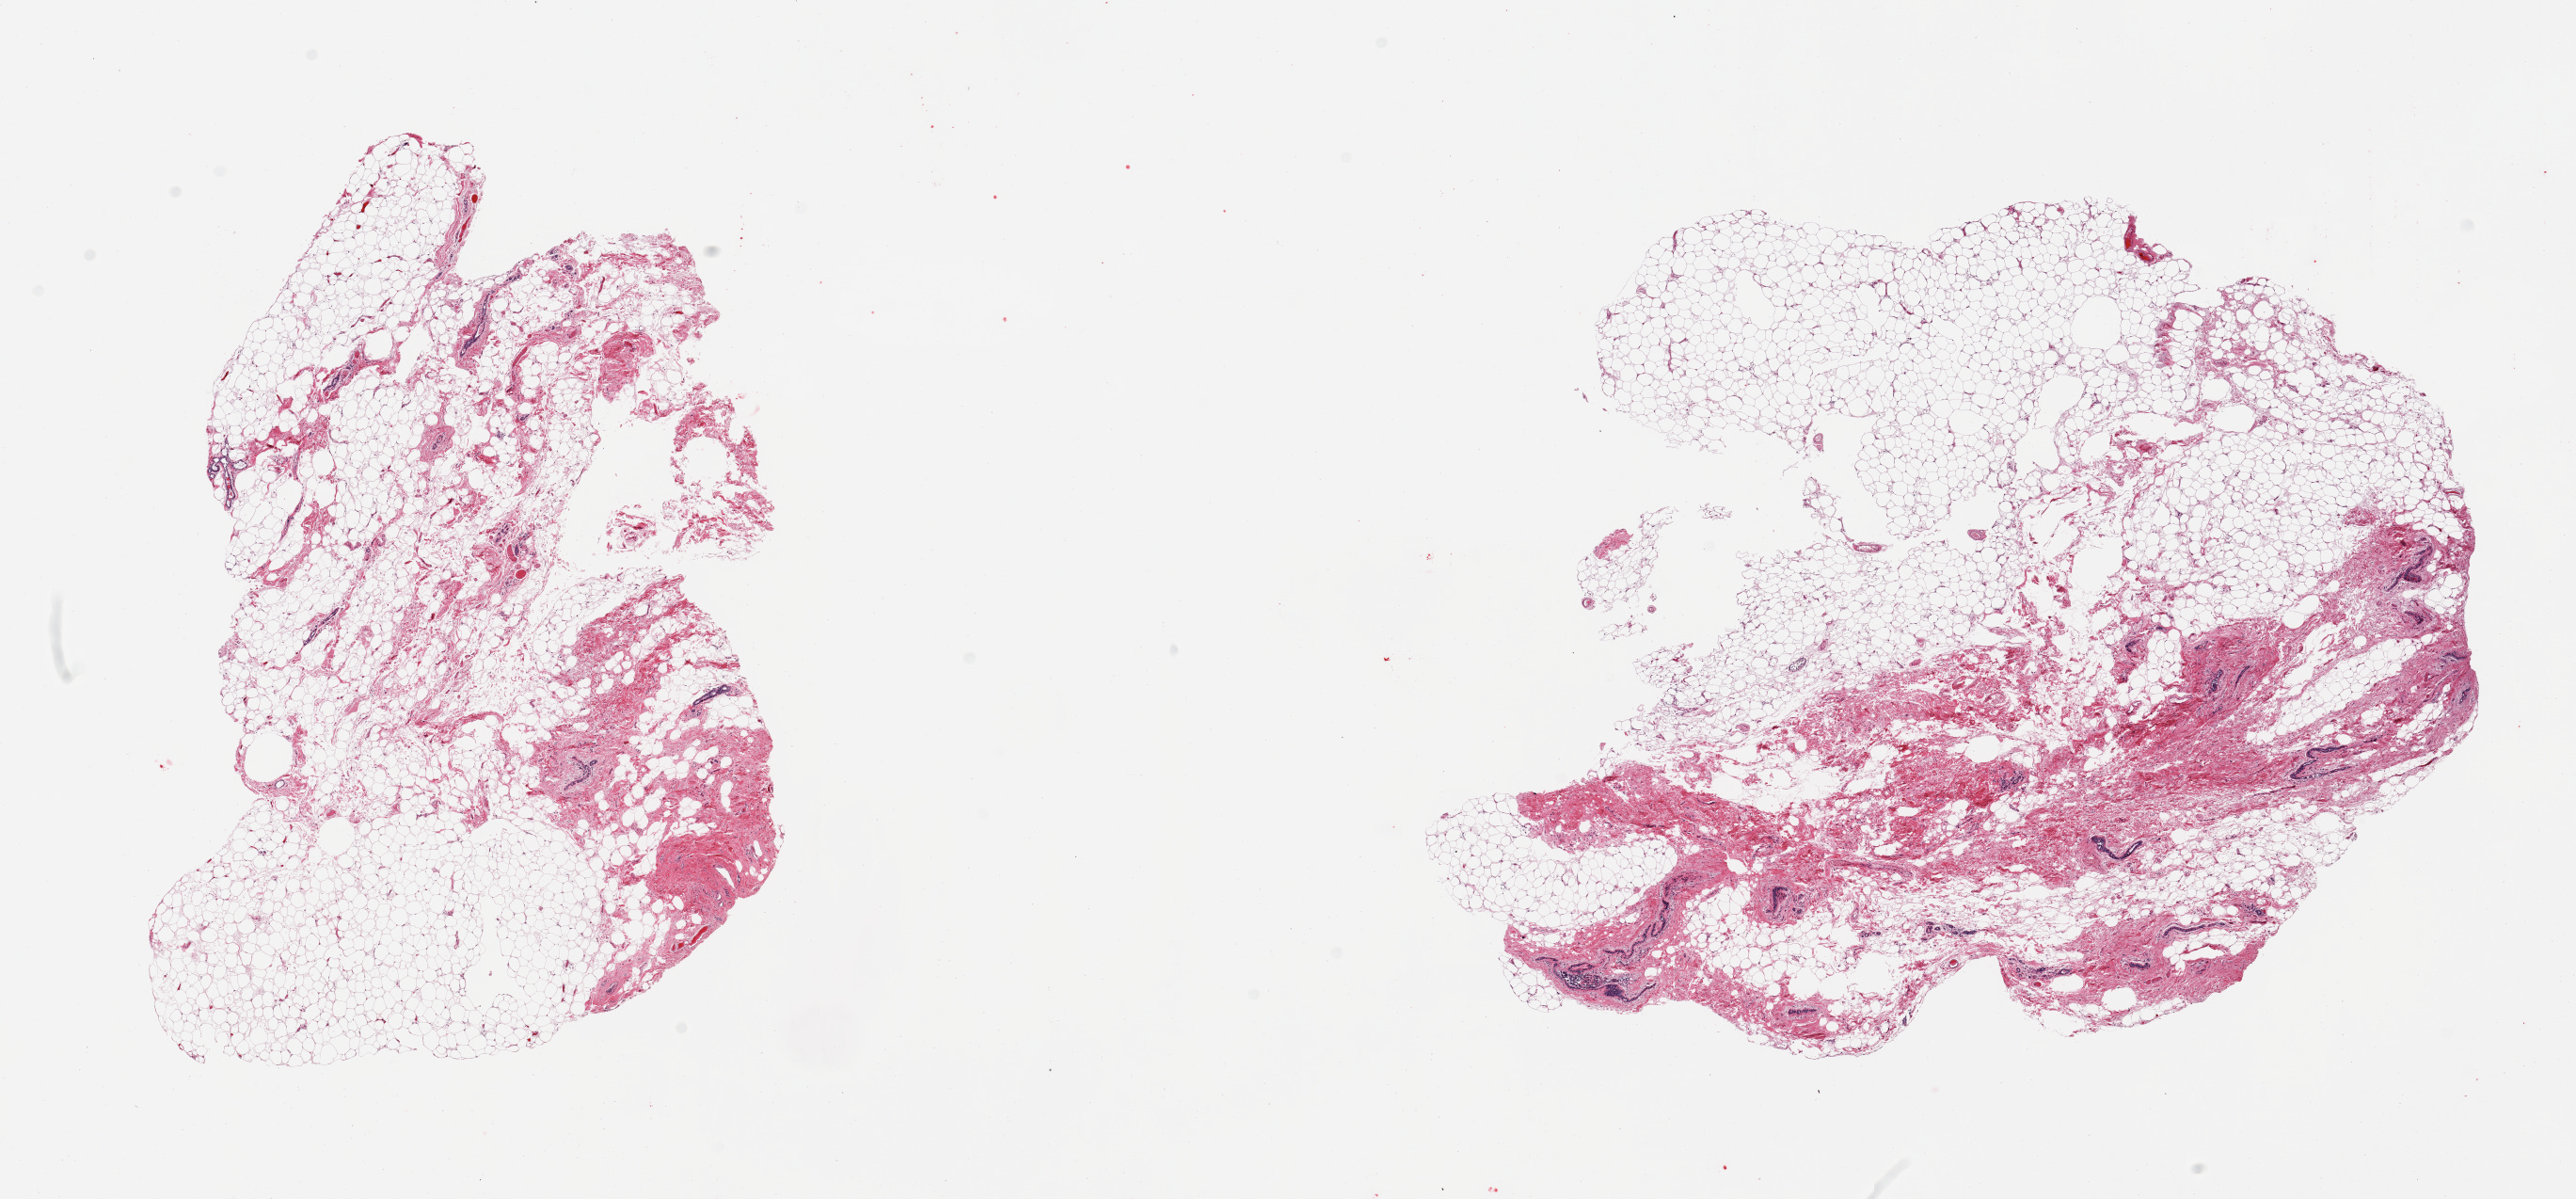
Whole-slide image, H&E stain — a low-resolution overview of the entire scanned area, about 21.7 x 10.1 mm (slide scanned at 20x), PAXgene-fixed paraffin-embedded (PFPE) section, sampled site (target tissue): breast, donor tissue sample. Female donor.
Reviewer comment on this tissue sample: 2 pieces; predominantly mature adipose tissue with fibrous stroma with scattered ducts and scant atrophic lobules.